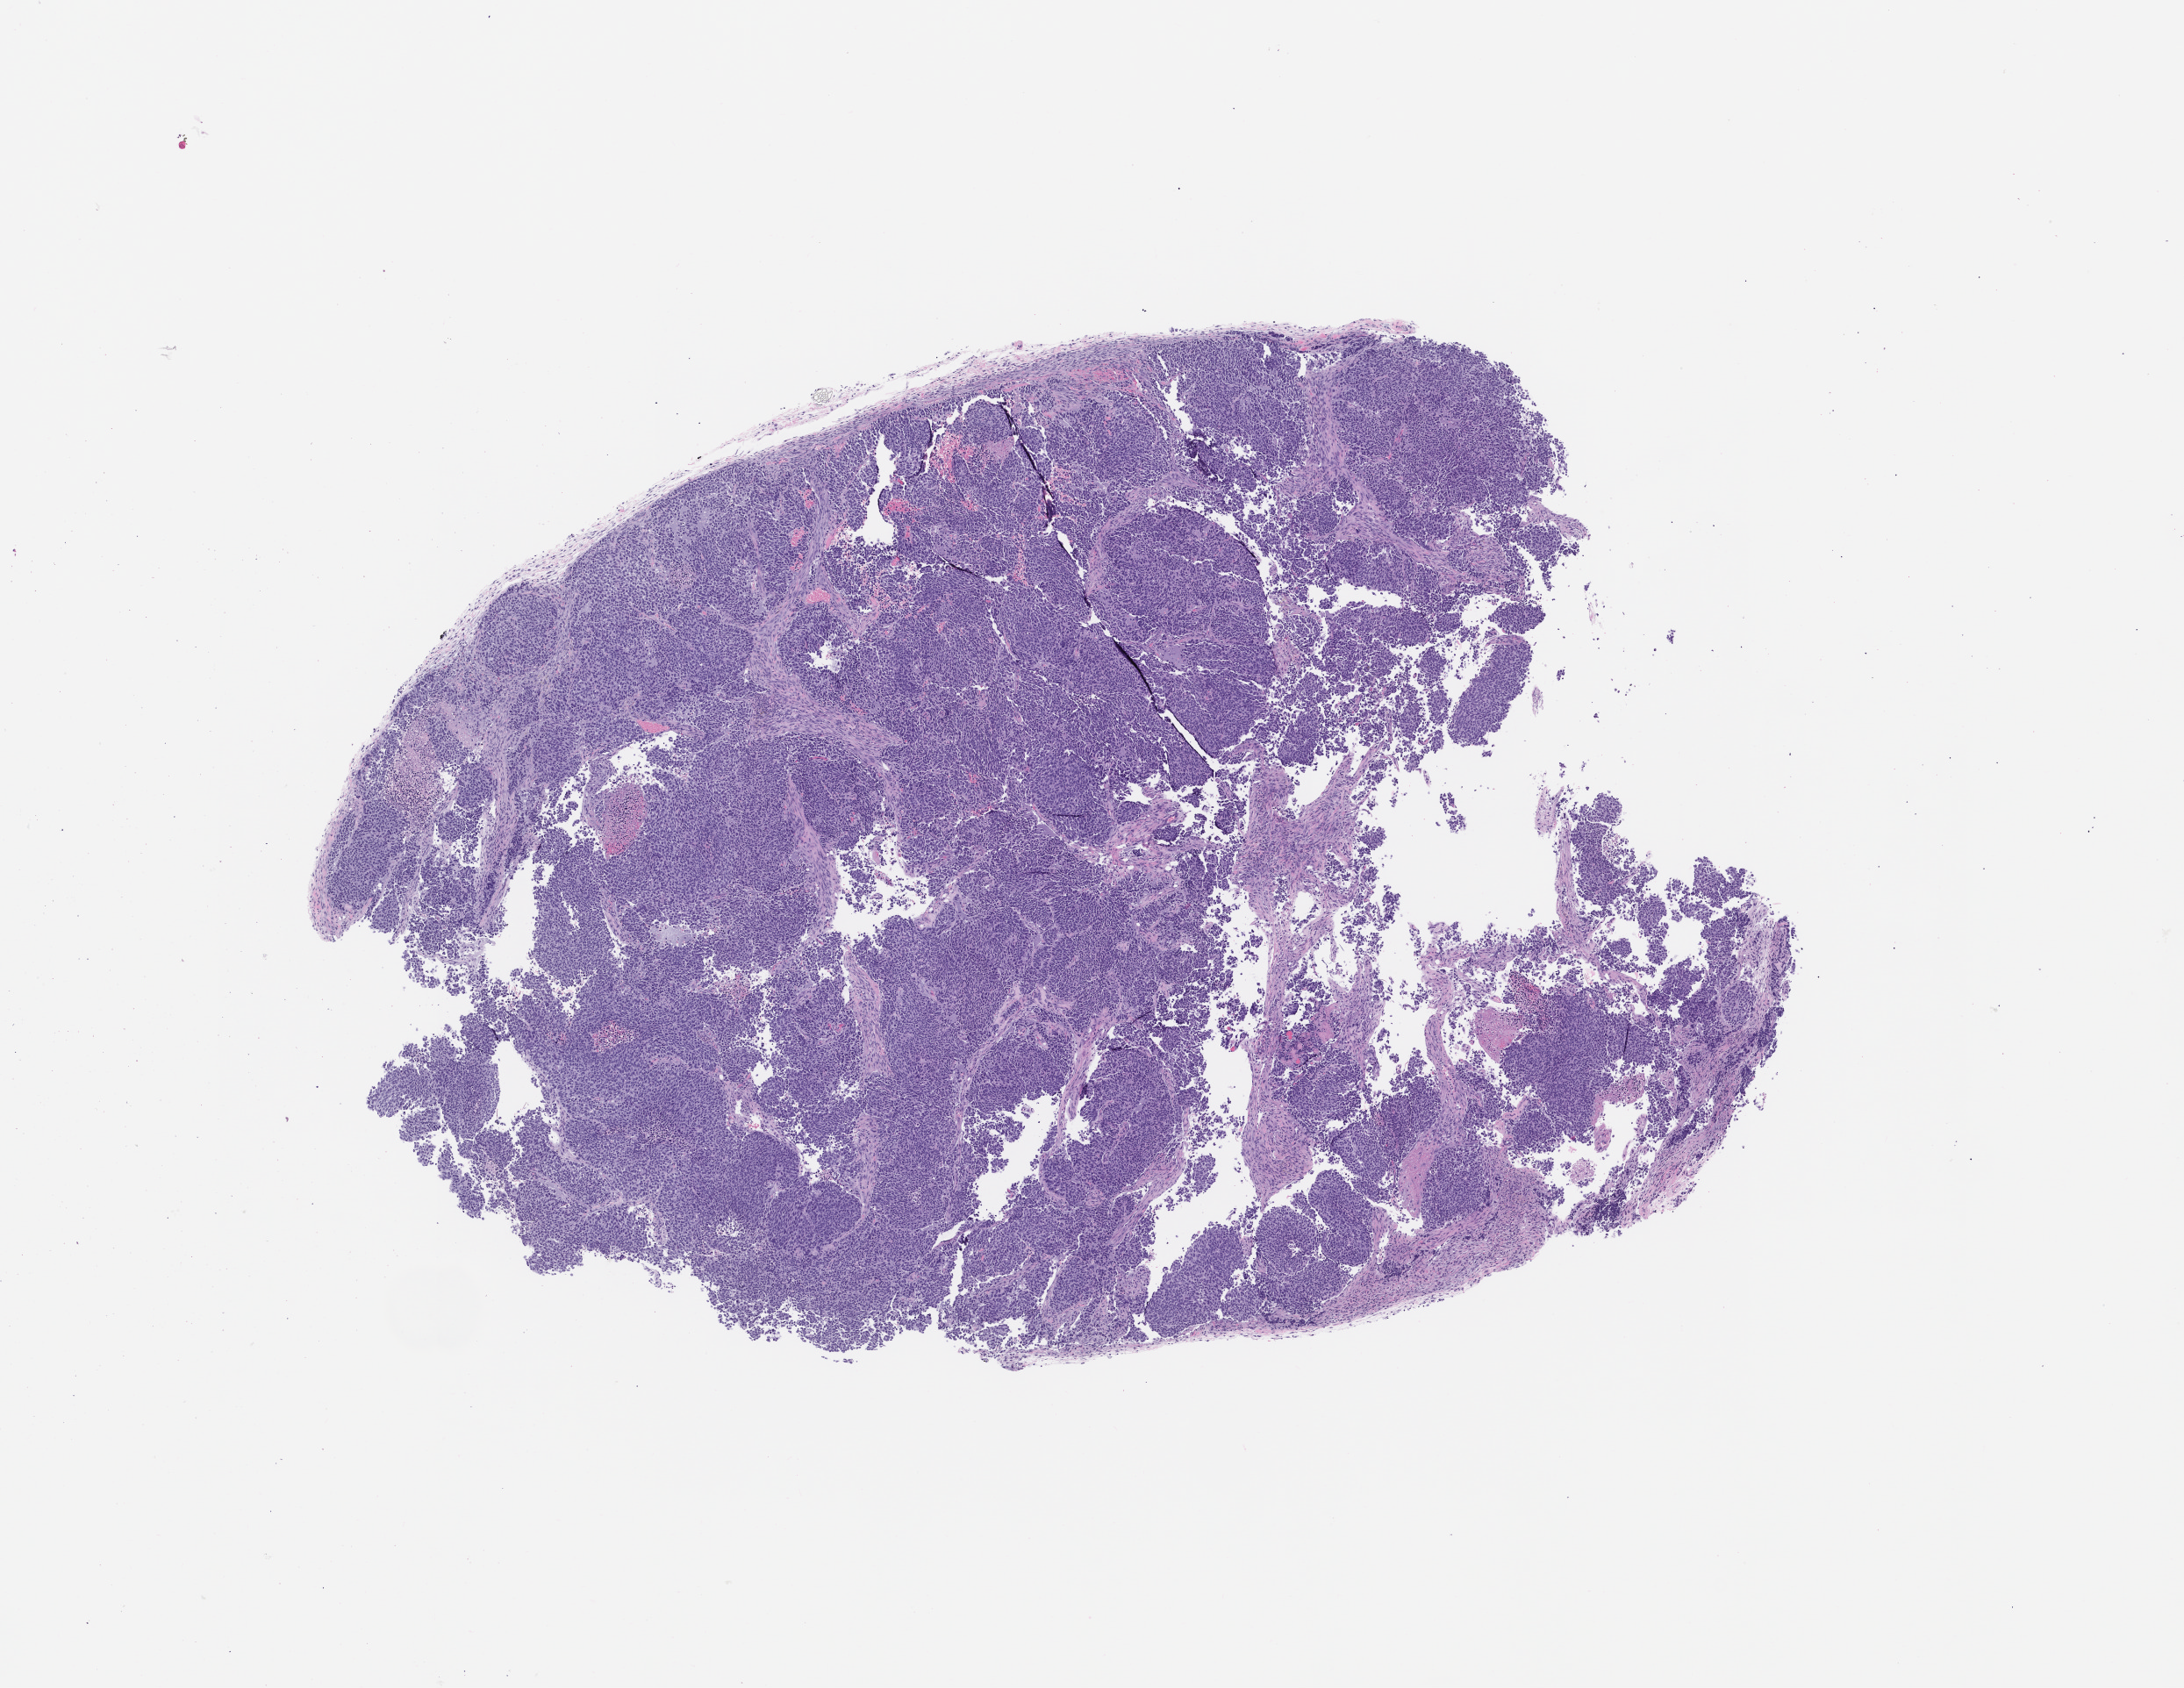
Whole-slide image, H&E: patient-derived xenograft (human tumor grown in a mouse), a low-resolution overview of the entire scanned area, about 10.0 x 7.7 mm. Formalin-fixed paraffin-embedded section. Originating tumor site category: lung.
Originating patient diagnosis: Lung Adenocarcinoma.